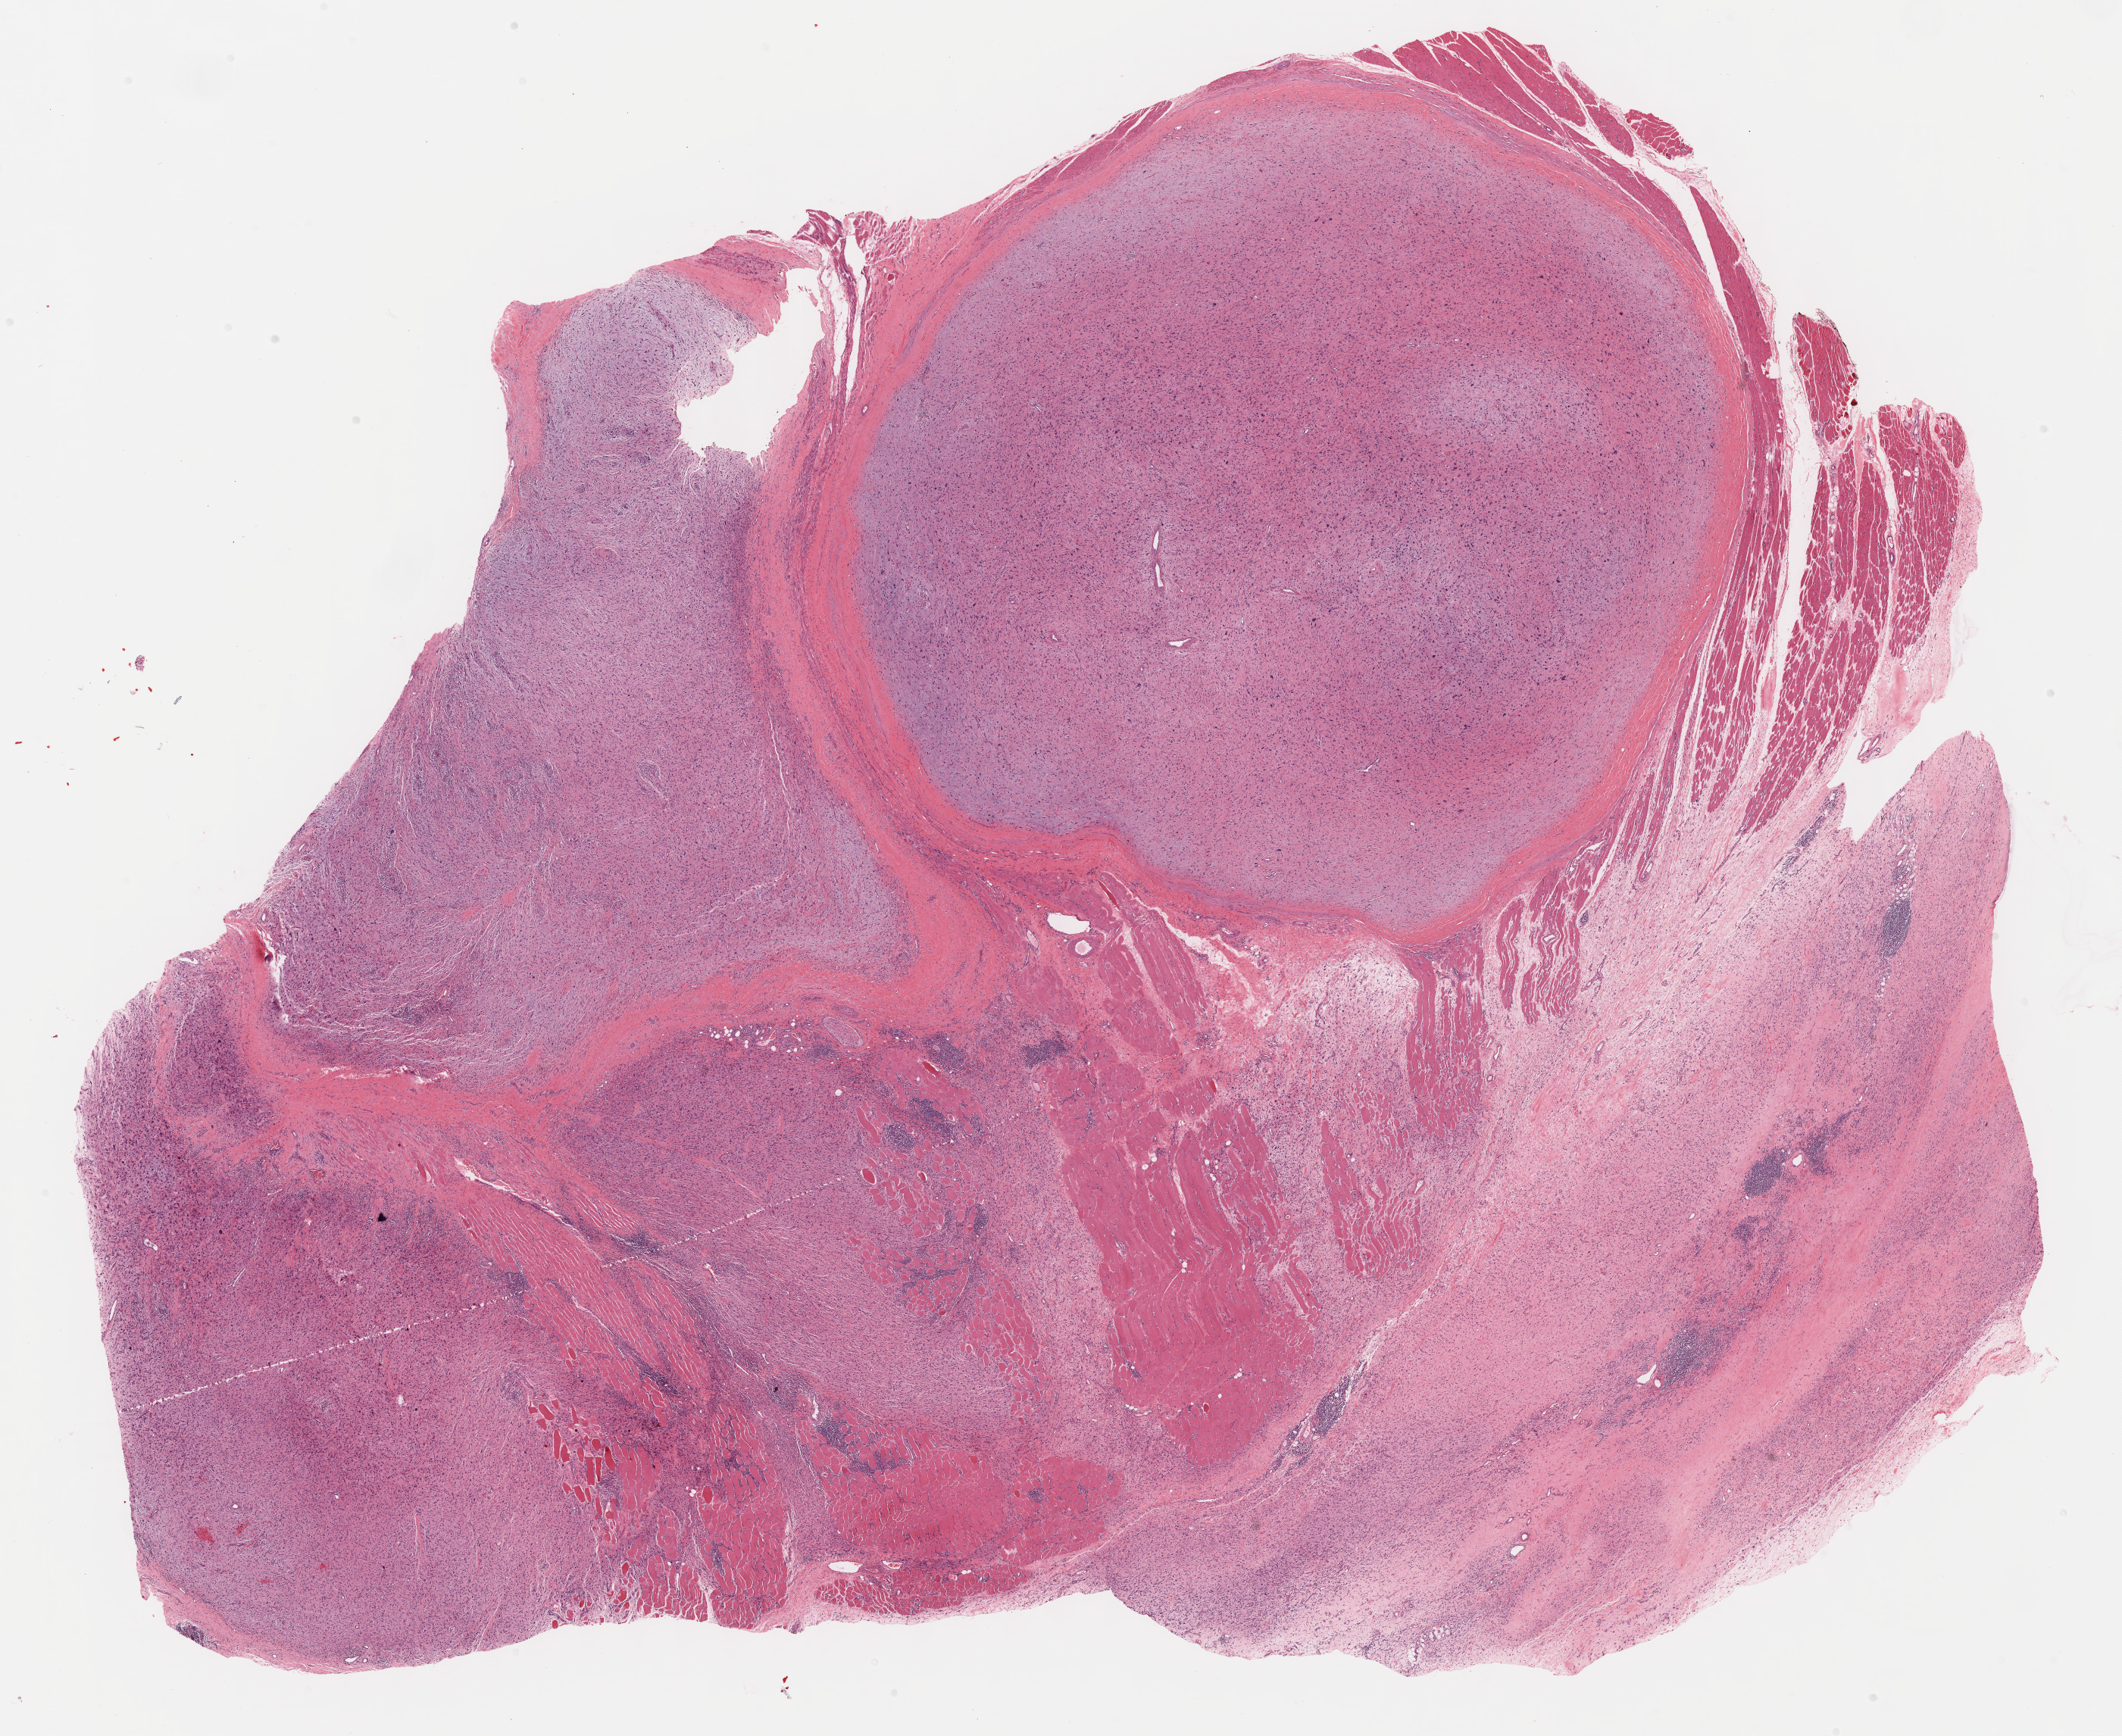
Digitized Hematoxylin and eosin (H&E) stained tissue section (whole slide) — shown as a low-resolution overview of the whole scanned area (about 22.7 x 18.5 mm, from a 40x scan); FFPE section; primary tumour sample from the connective, subcutaneous and other soft tissues. Patient: female, age at initial diagnosis 78 years.
Diagnosis: Fibromyxosarcoma.